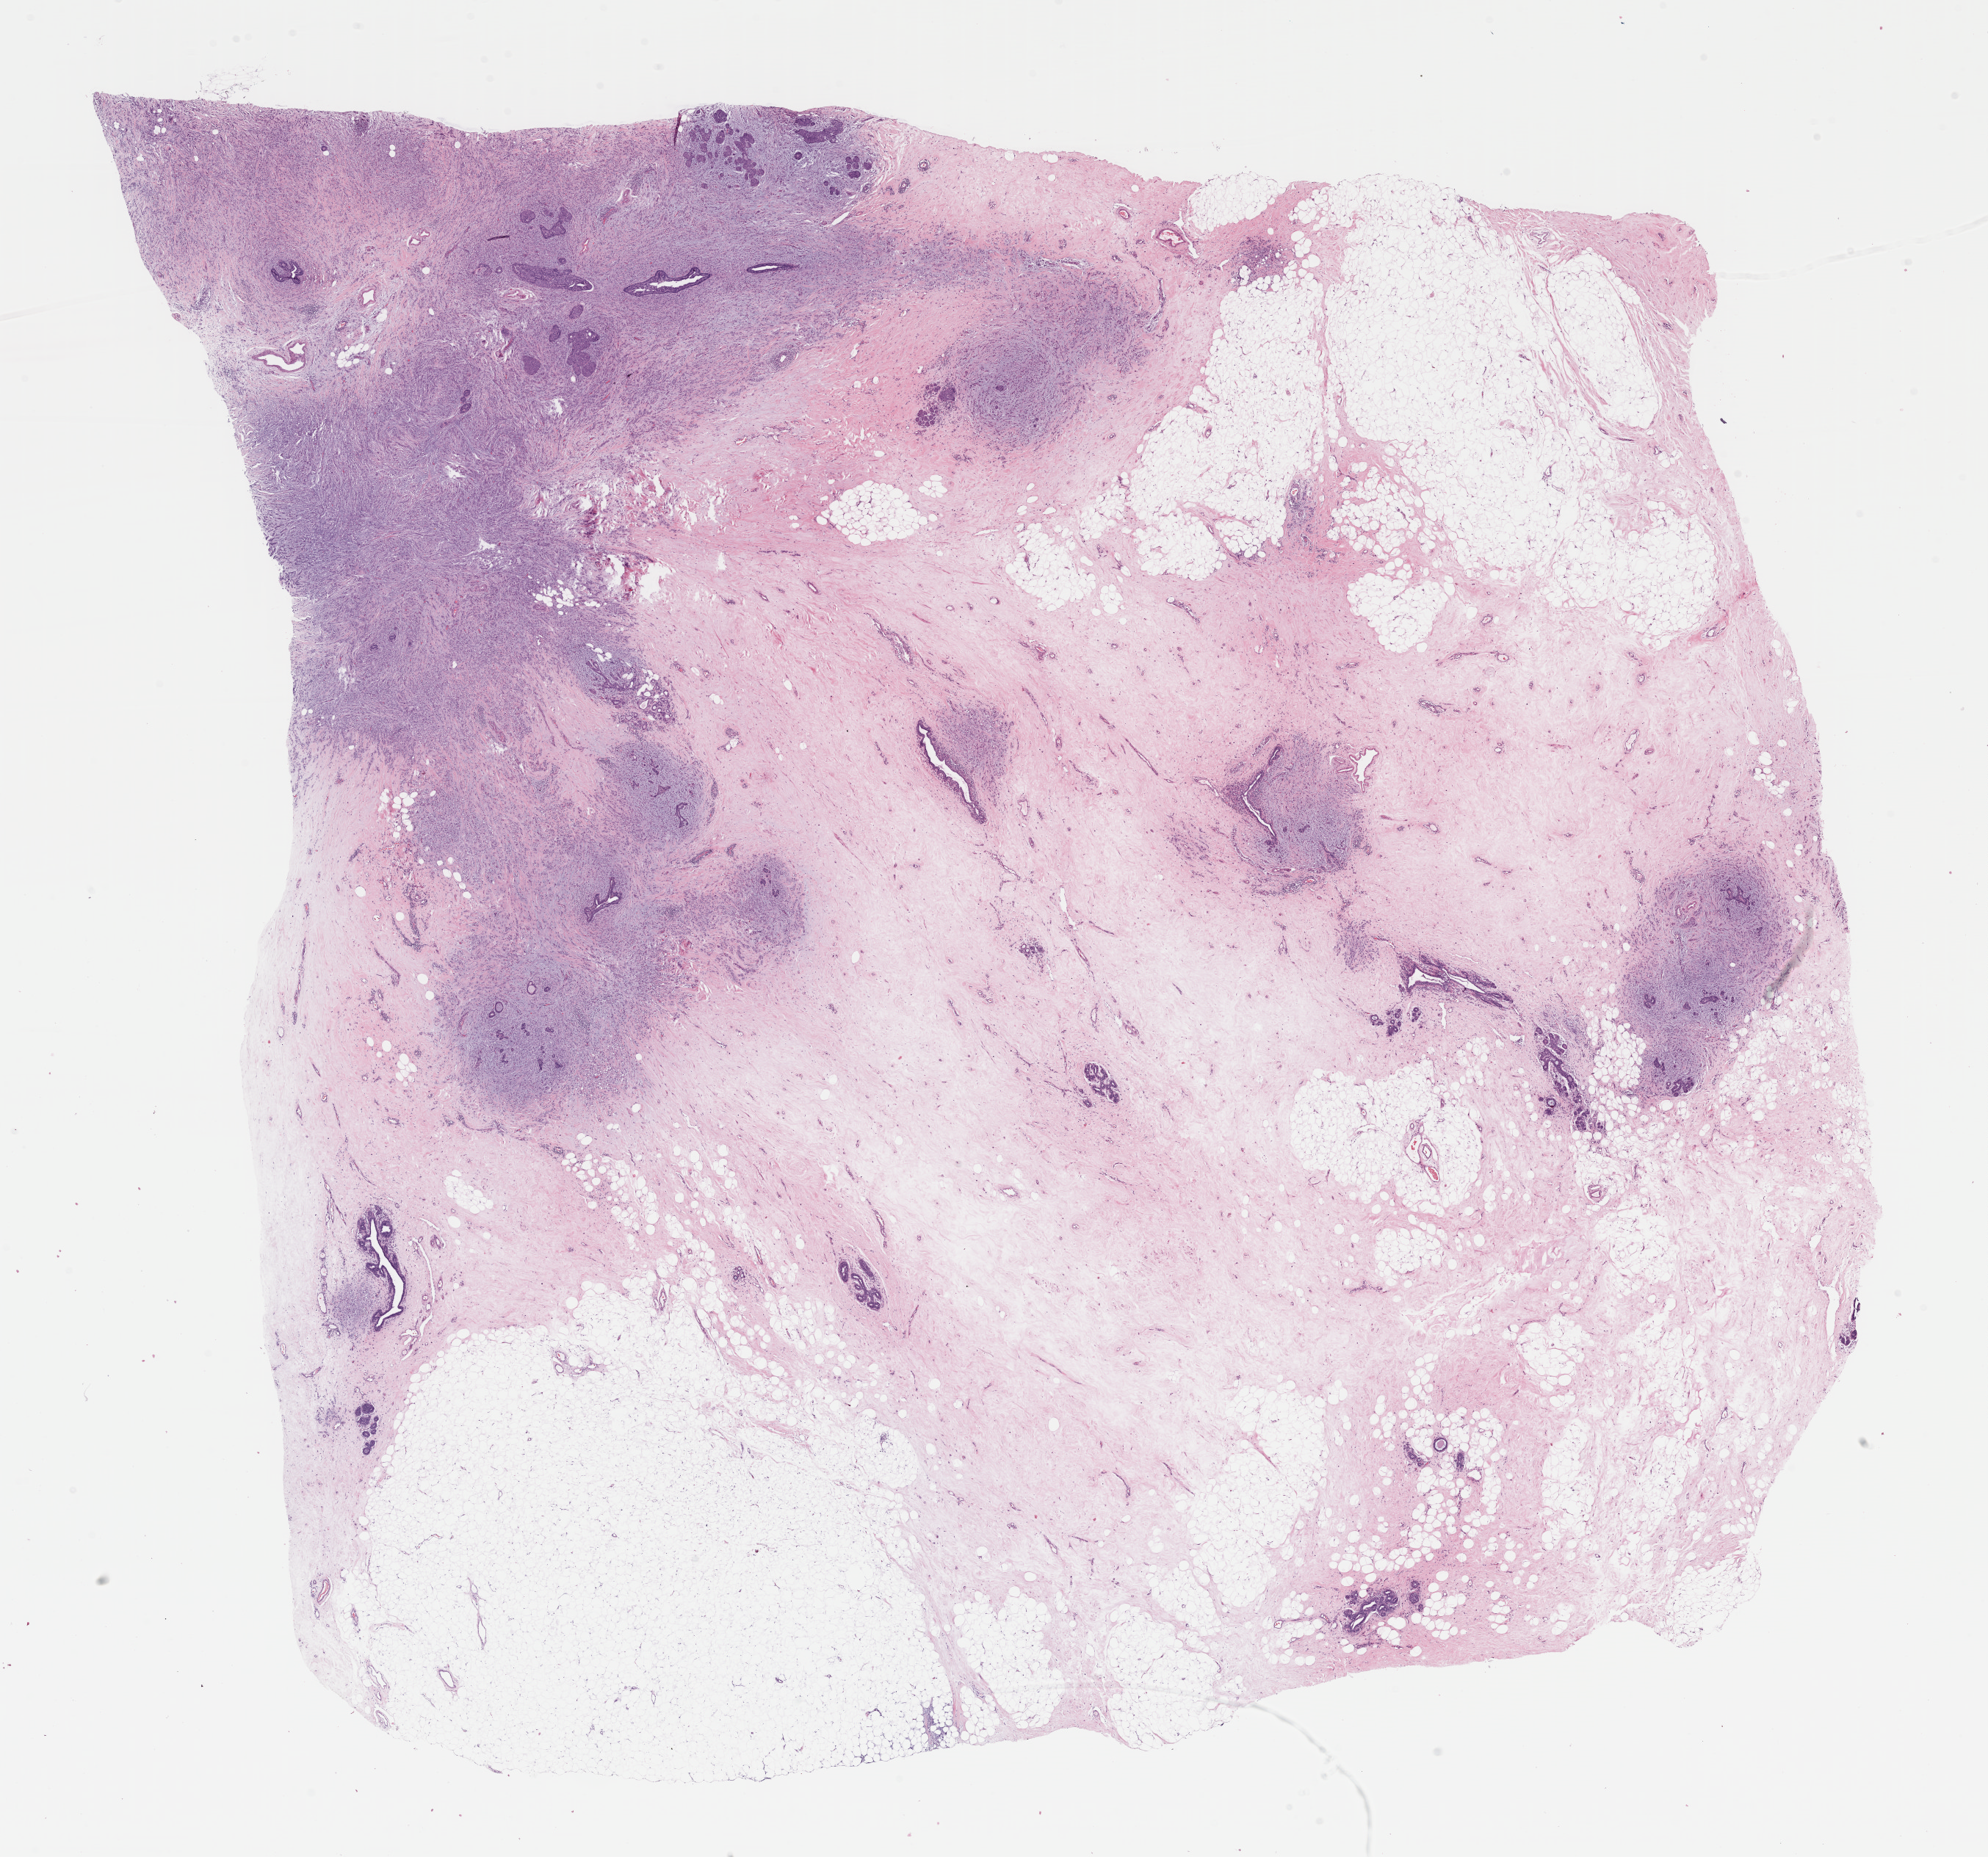
Digitized H&E tissue section (whole slide) — shown as a low-resolution overview of the whole scanned area (about 21.4 x 20.0 mm, from a 40x scan). Formalin-fixed paraffin-embedded (FFPE) diagnostic section. Breast, primary tumour sample. Patient: female, age at initial diagnosis 46 years.
* AJCC pathologic stage: IIIC (7th edition)
* pathologic diagnosis: Lobular carcinoma, NOS
* TNM: T3 N3a M0